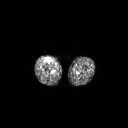
FDG PET of an extremity soft-tissue mass (from a PET/CT study), one axial slice; slice 238 of 311 in the series (ordered by position); 3.27 mm slice thickness; 128 × 128 image matrix, field of view 700 × 700 mm. Patient: male, 56 years. Case-level facts recorded for this patient, not image findings: histological type: pleiomorphic leiomyosarcoma; grade: intermediate; site of the primary tumour: right thigh.
Annotated regions visible in this slice (expert contour drawn on MRI and transferred to this co-registered scan by the dataset authors):
- gross tumour volume including surrounding oedema: bounding box (x1, y1, x2, y2) in pixels: (45, 58, 51, 62)